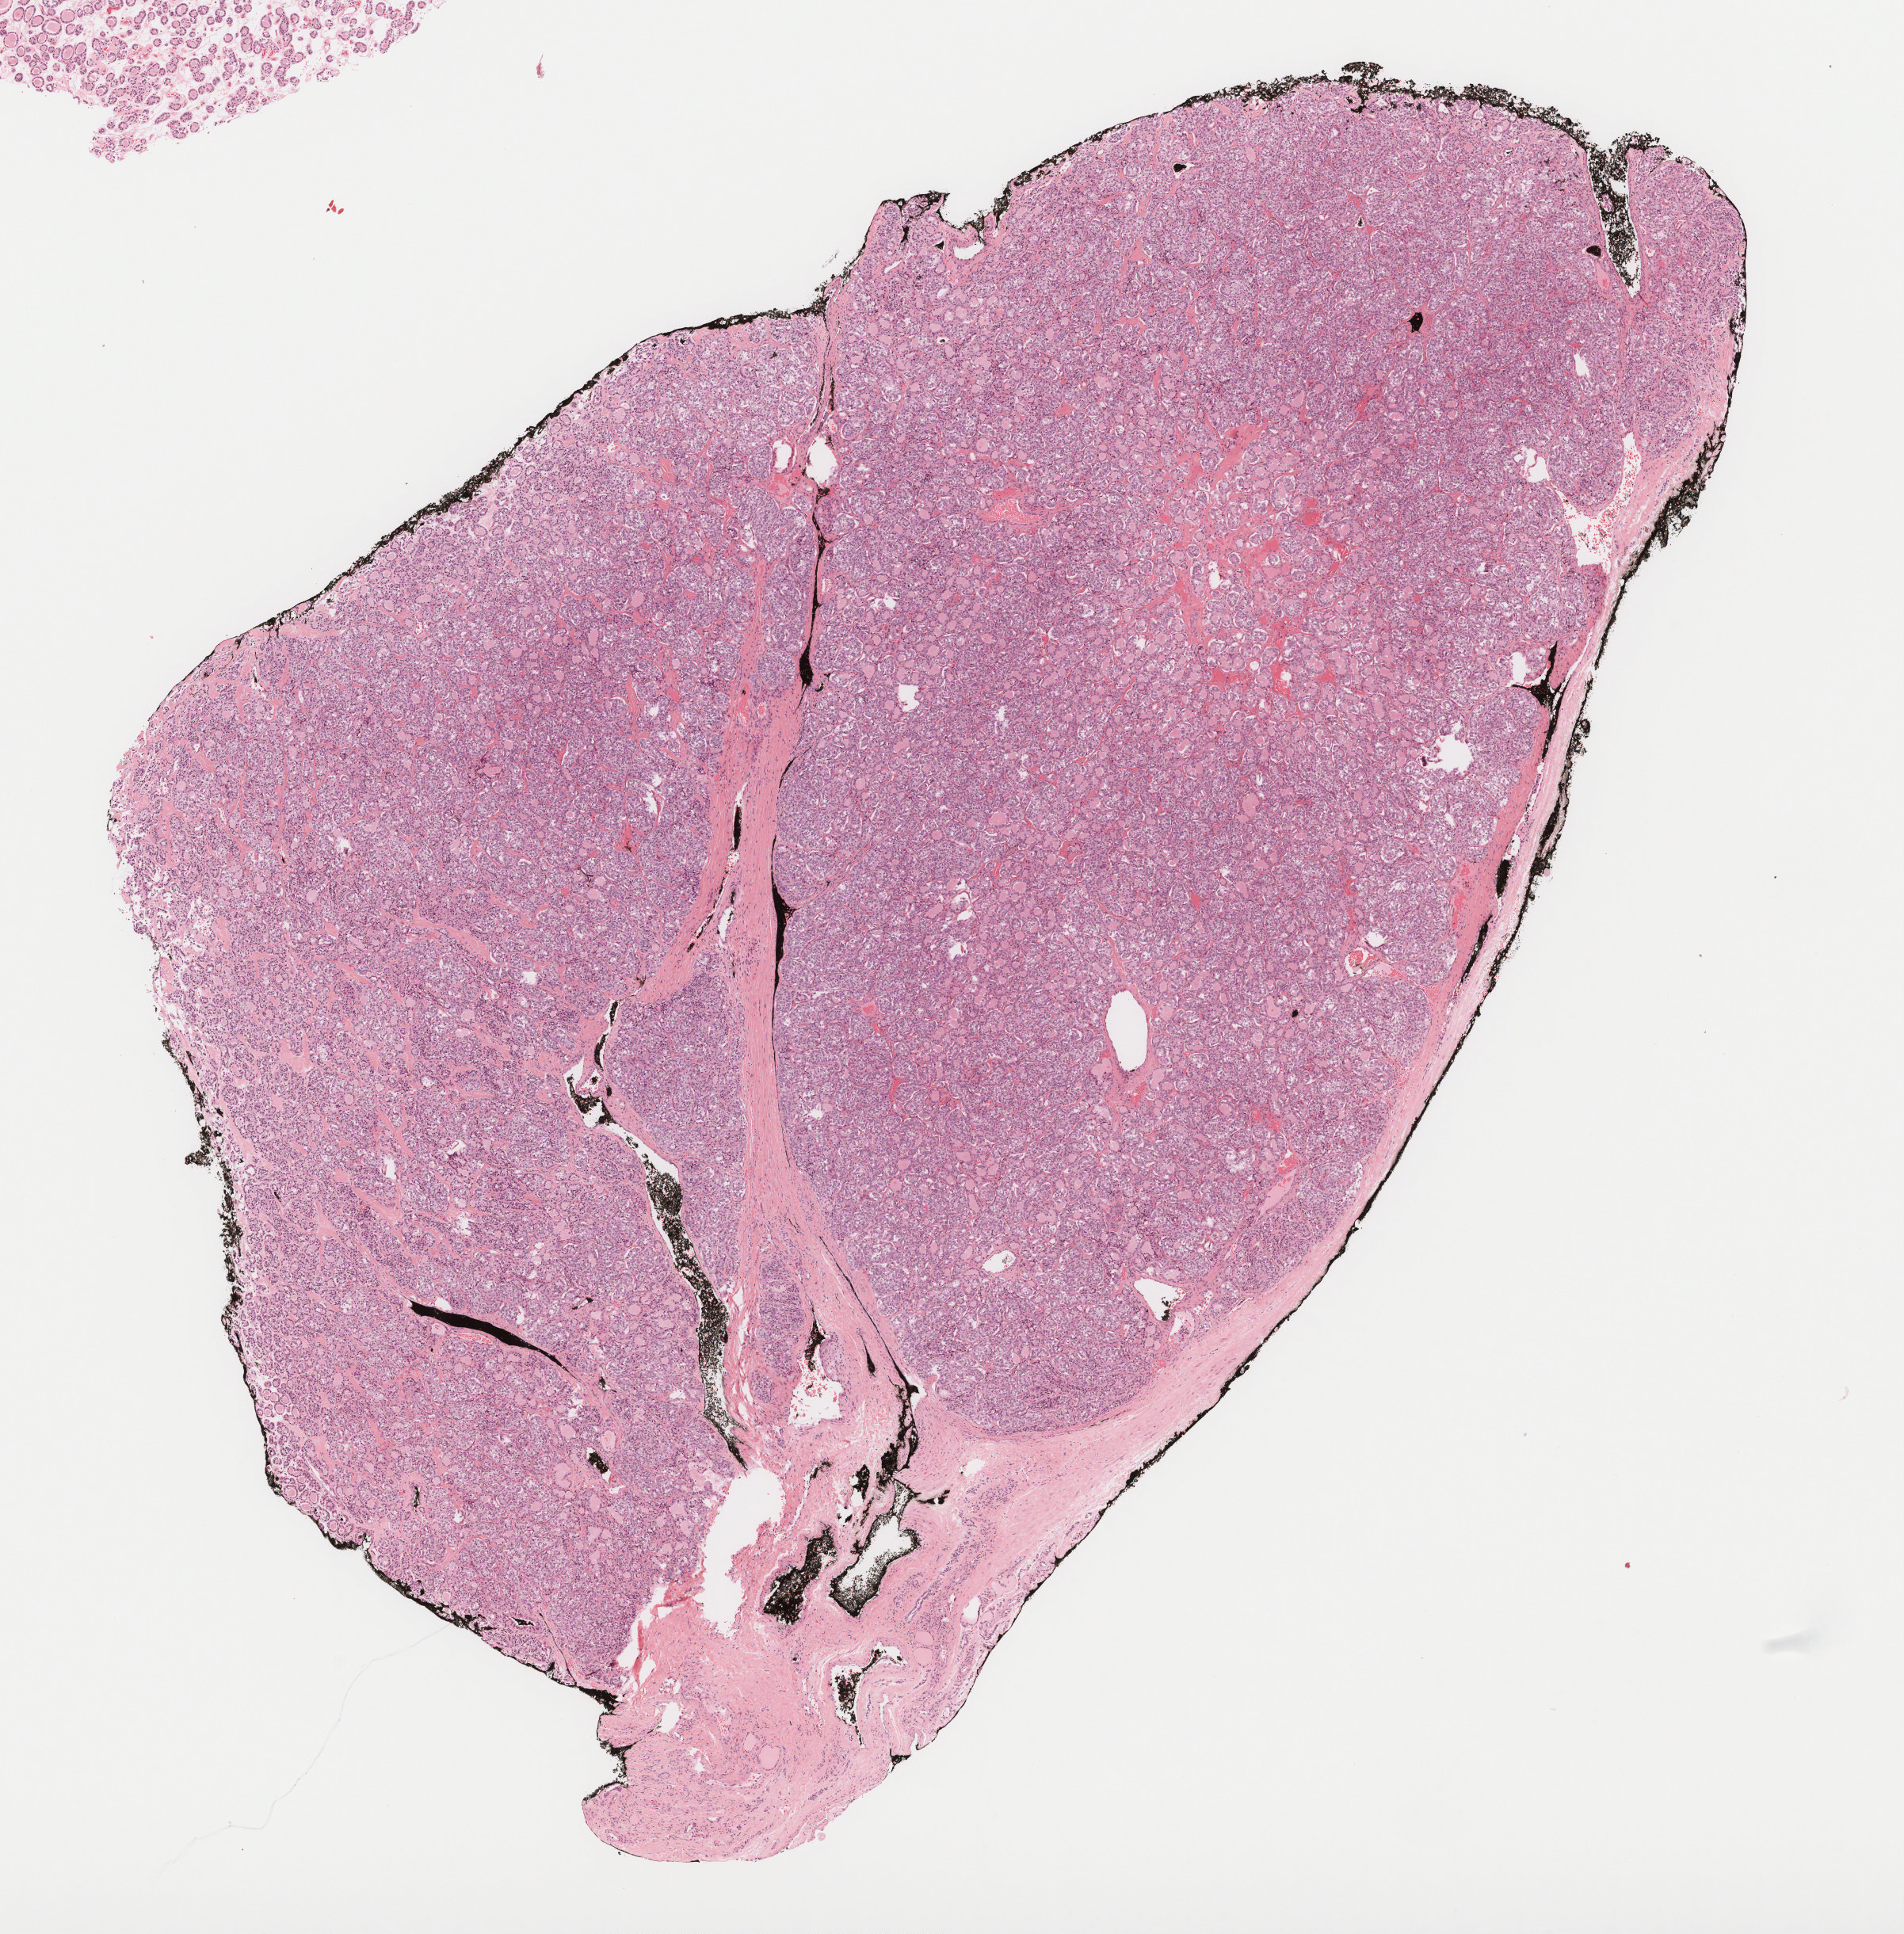
Whole-slide histology image, H&E-stained — whole scanned area (about 9.7 x 9.8 mm) shown as a low-resolution overview, formalin-fixed paraffin-embedded (FFPE) diagnostic section, sample: primary tumour, thyroid. Male patient; age at initial diagnosis 46 years.
Pathologic diagnosis: Papillary carcinoma, follicular variant (thyroid gland).